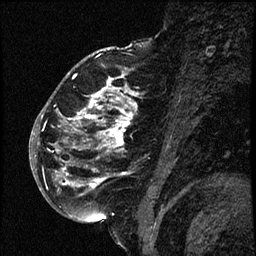
Breast MRI (dynamic contrast-enhanced), one sagittal slice; position 36 of 66 along the scan axis; dynamic contrast-enhanced study with each time point stored as its own series, time point 2 of 3 at this slice position (early post-contrast, ordered by acquisition time); 1.5 T; TE 4.2 ms, TR 17.6 ms; 2 mm slice thickness; 256 × 256 image matrix, field of view 200 × 200 mm. Female patient. Case-level facts recorded for this patient, not image findings: setting: breast cancer imaged before/during neoadjuvant chemotherapy; receptor status: HER2-positive.
Outlined on this slice (semi-automatic segmentation, software-assisted and operator-edited):
- analysis volume of interest (the breast-tissue region the enhancement analysis was run in; not a lesion): bounding box (x1, y1, x2, y2) in pixels: (52, 69, 149, 209)
- tumour enhancement mask (voxels above the 100 % enhancement threshold inside the analysis volume of interest): (55, 78, 137, 188)